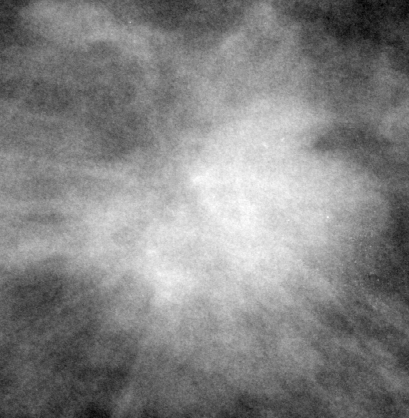
Crop from a digitized film mammogram around one marked abnormality; right breast; CC view; BI-RADS breast density category 1 (scale 1–4).
Mass, shape irregular, margins spiculated; BI-RADS assessment category 5; pathology (as recorded): malignant.